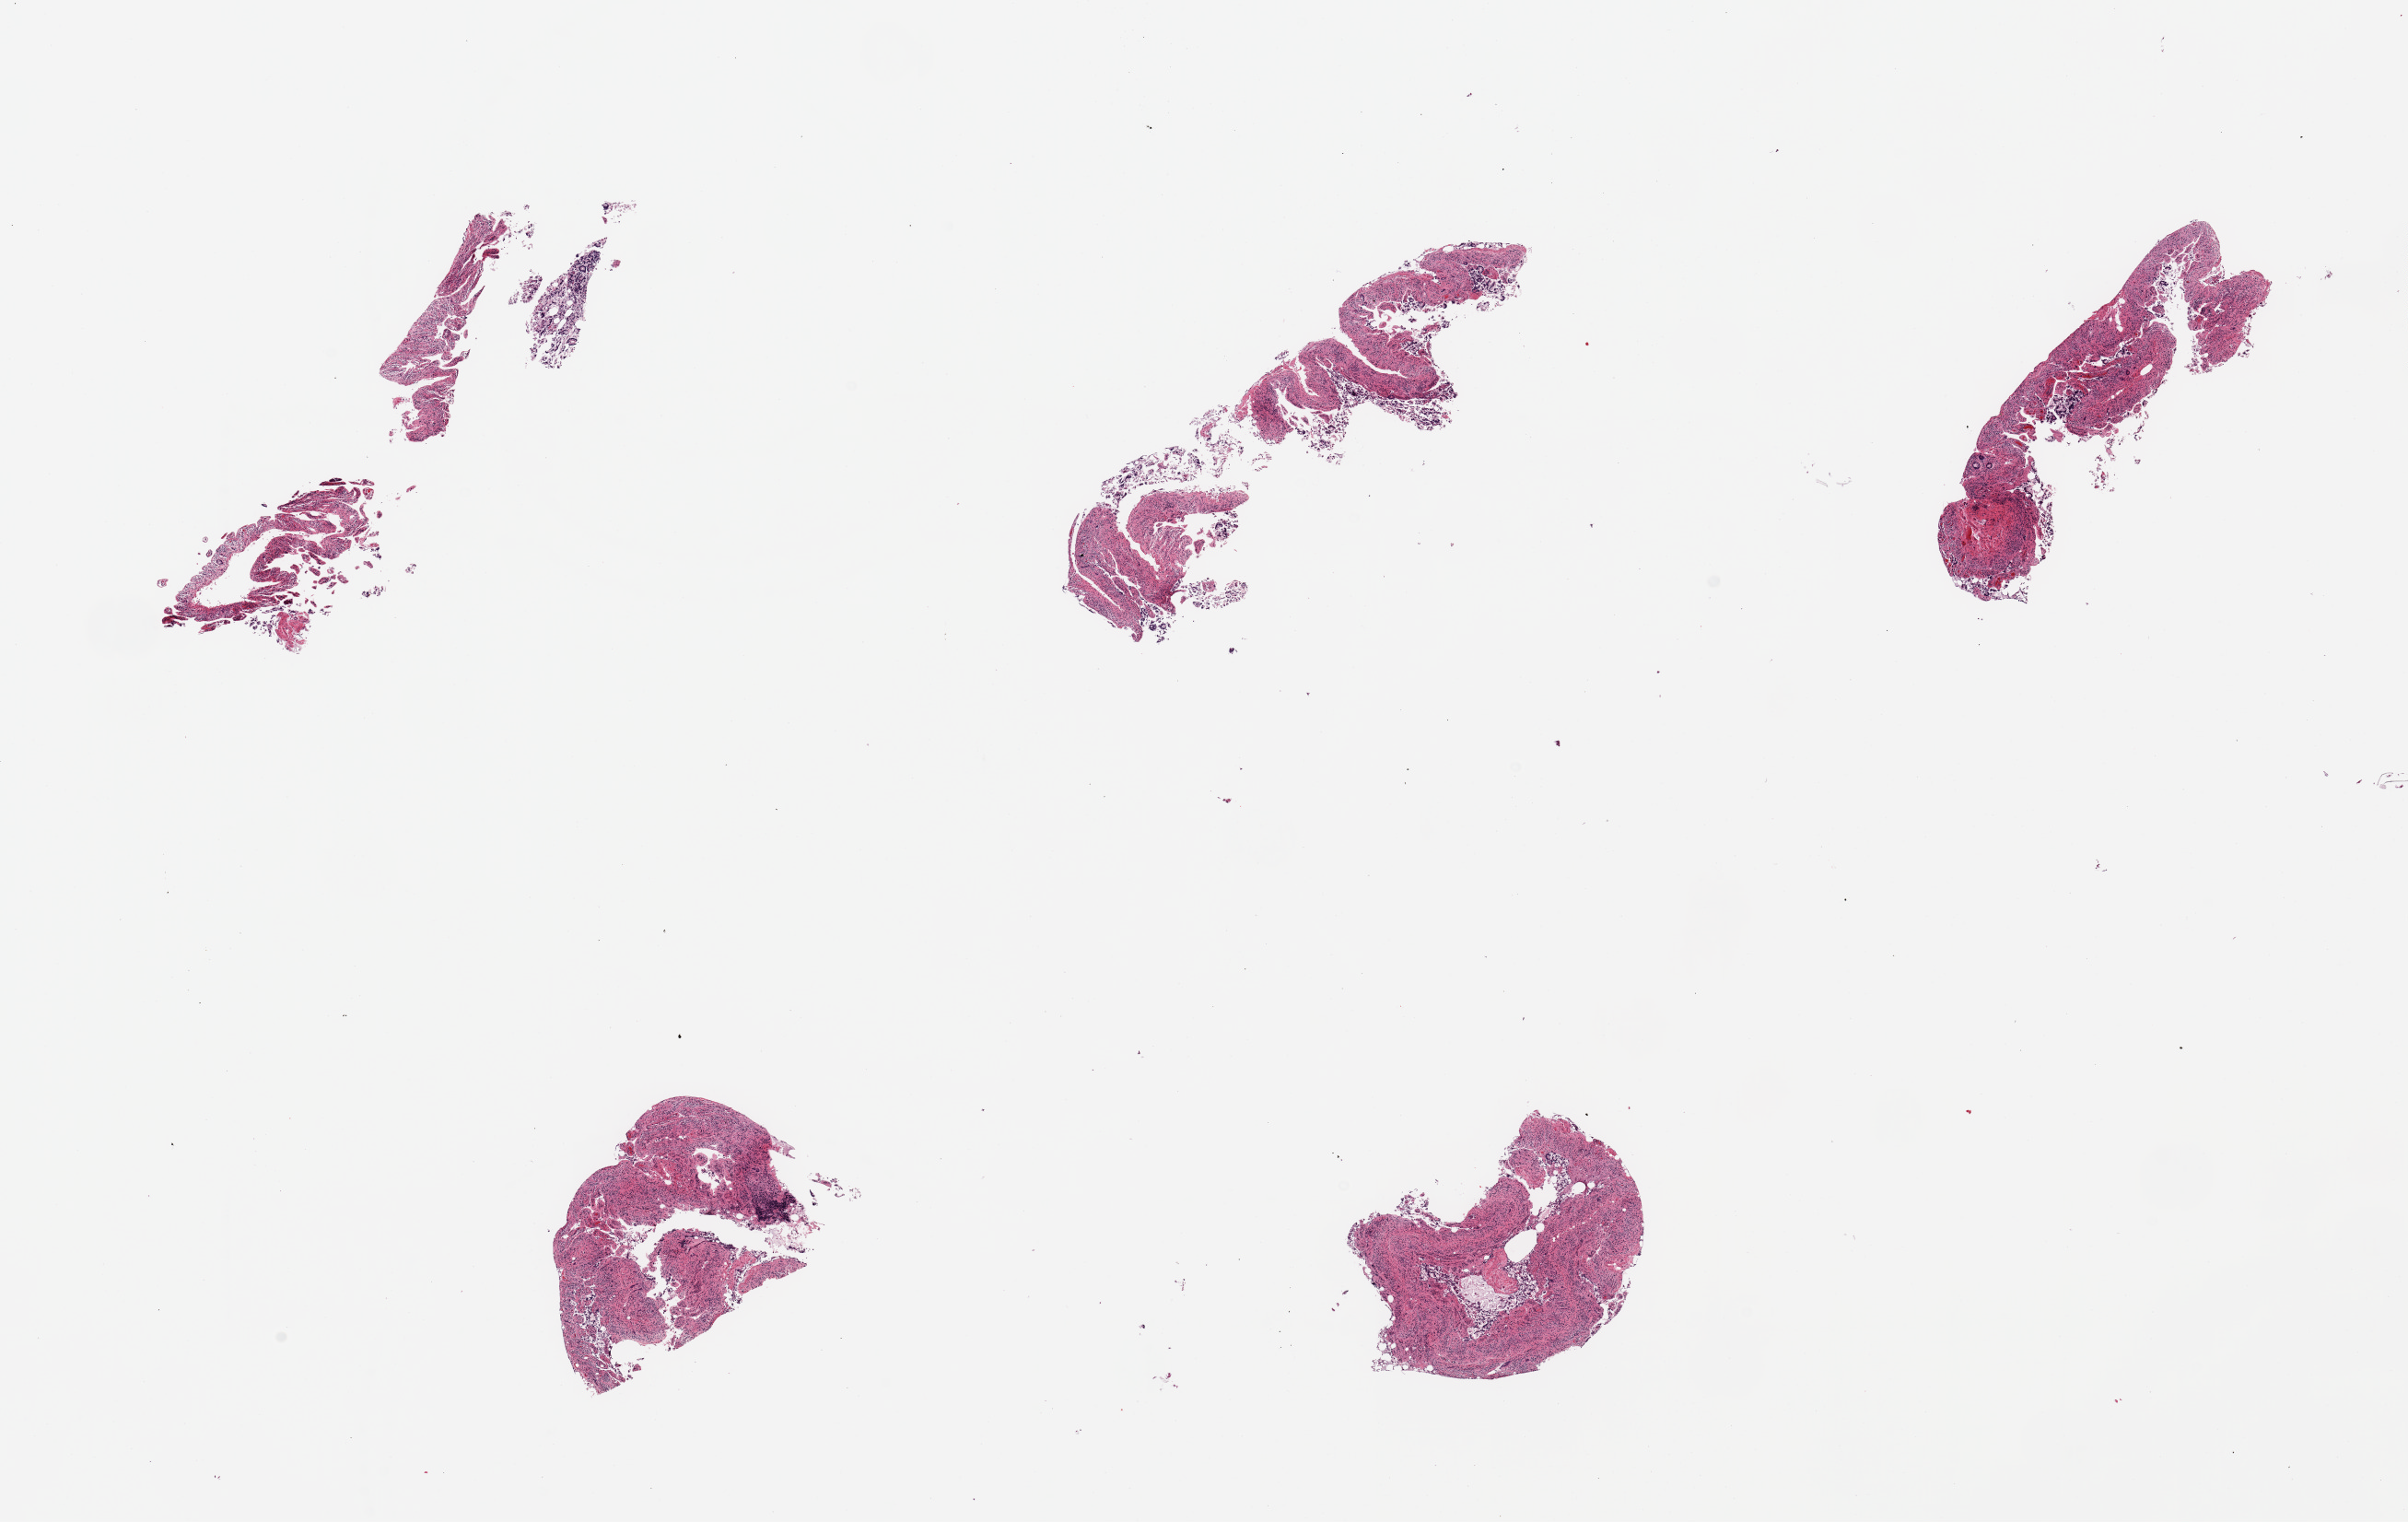
Hematoxylin and eosin (H&E) whole-slide image, brightfield — whole scanned area (about 20.7 x 13.1 mm, acquisition: 20x scan) shown as a low-resolution overview; PAXgene-fixed, paraffin-embedded tissue; target tissue: ileum; tissue donor sample. Male donor.
Pathologist's review note for this sample: 5 pieces, mucosa, trace lymphoid cells, no aggregates.